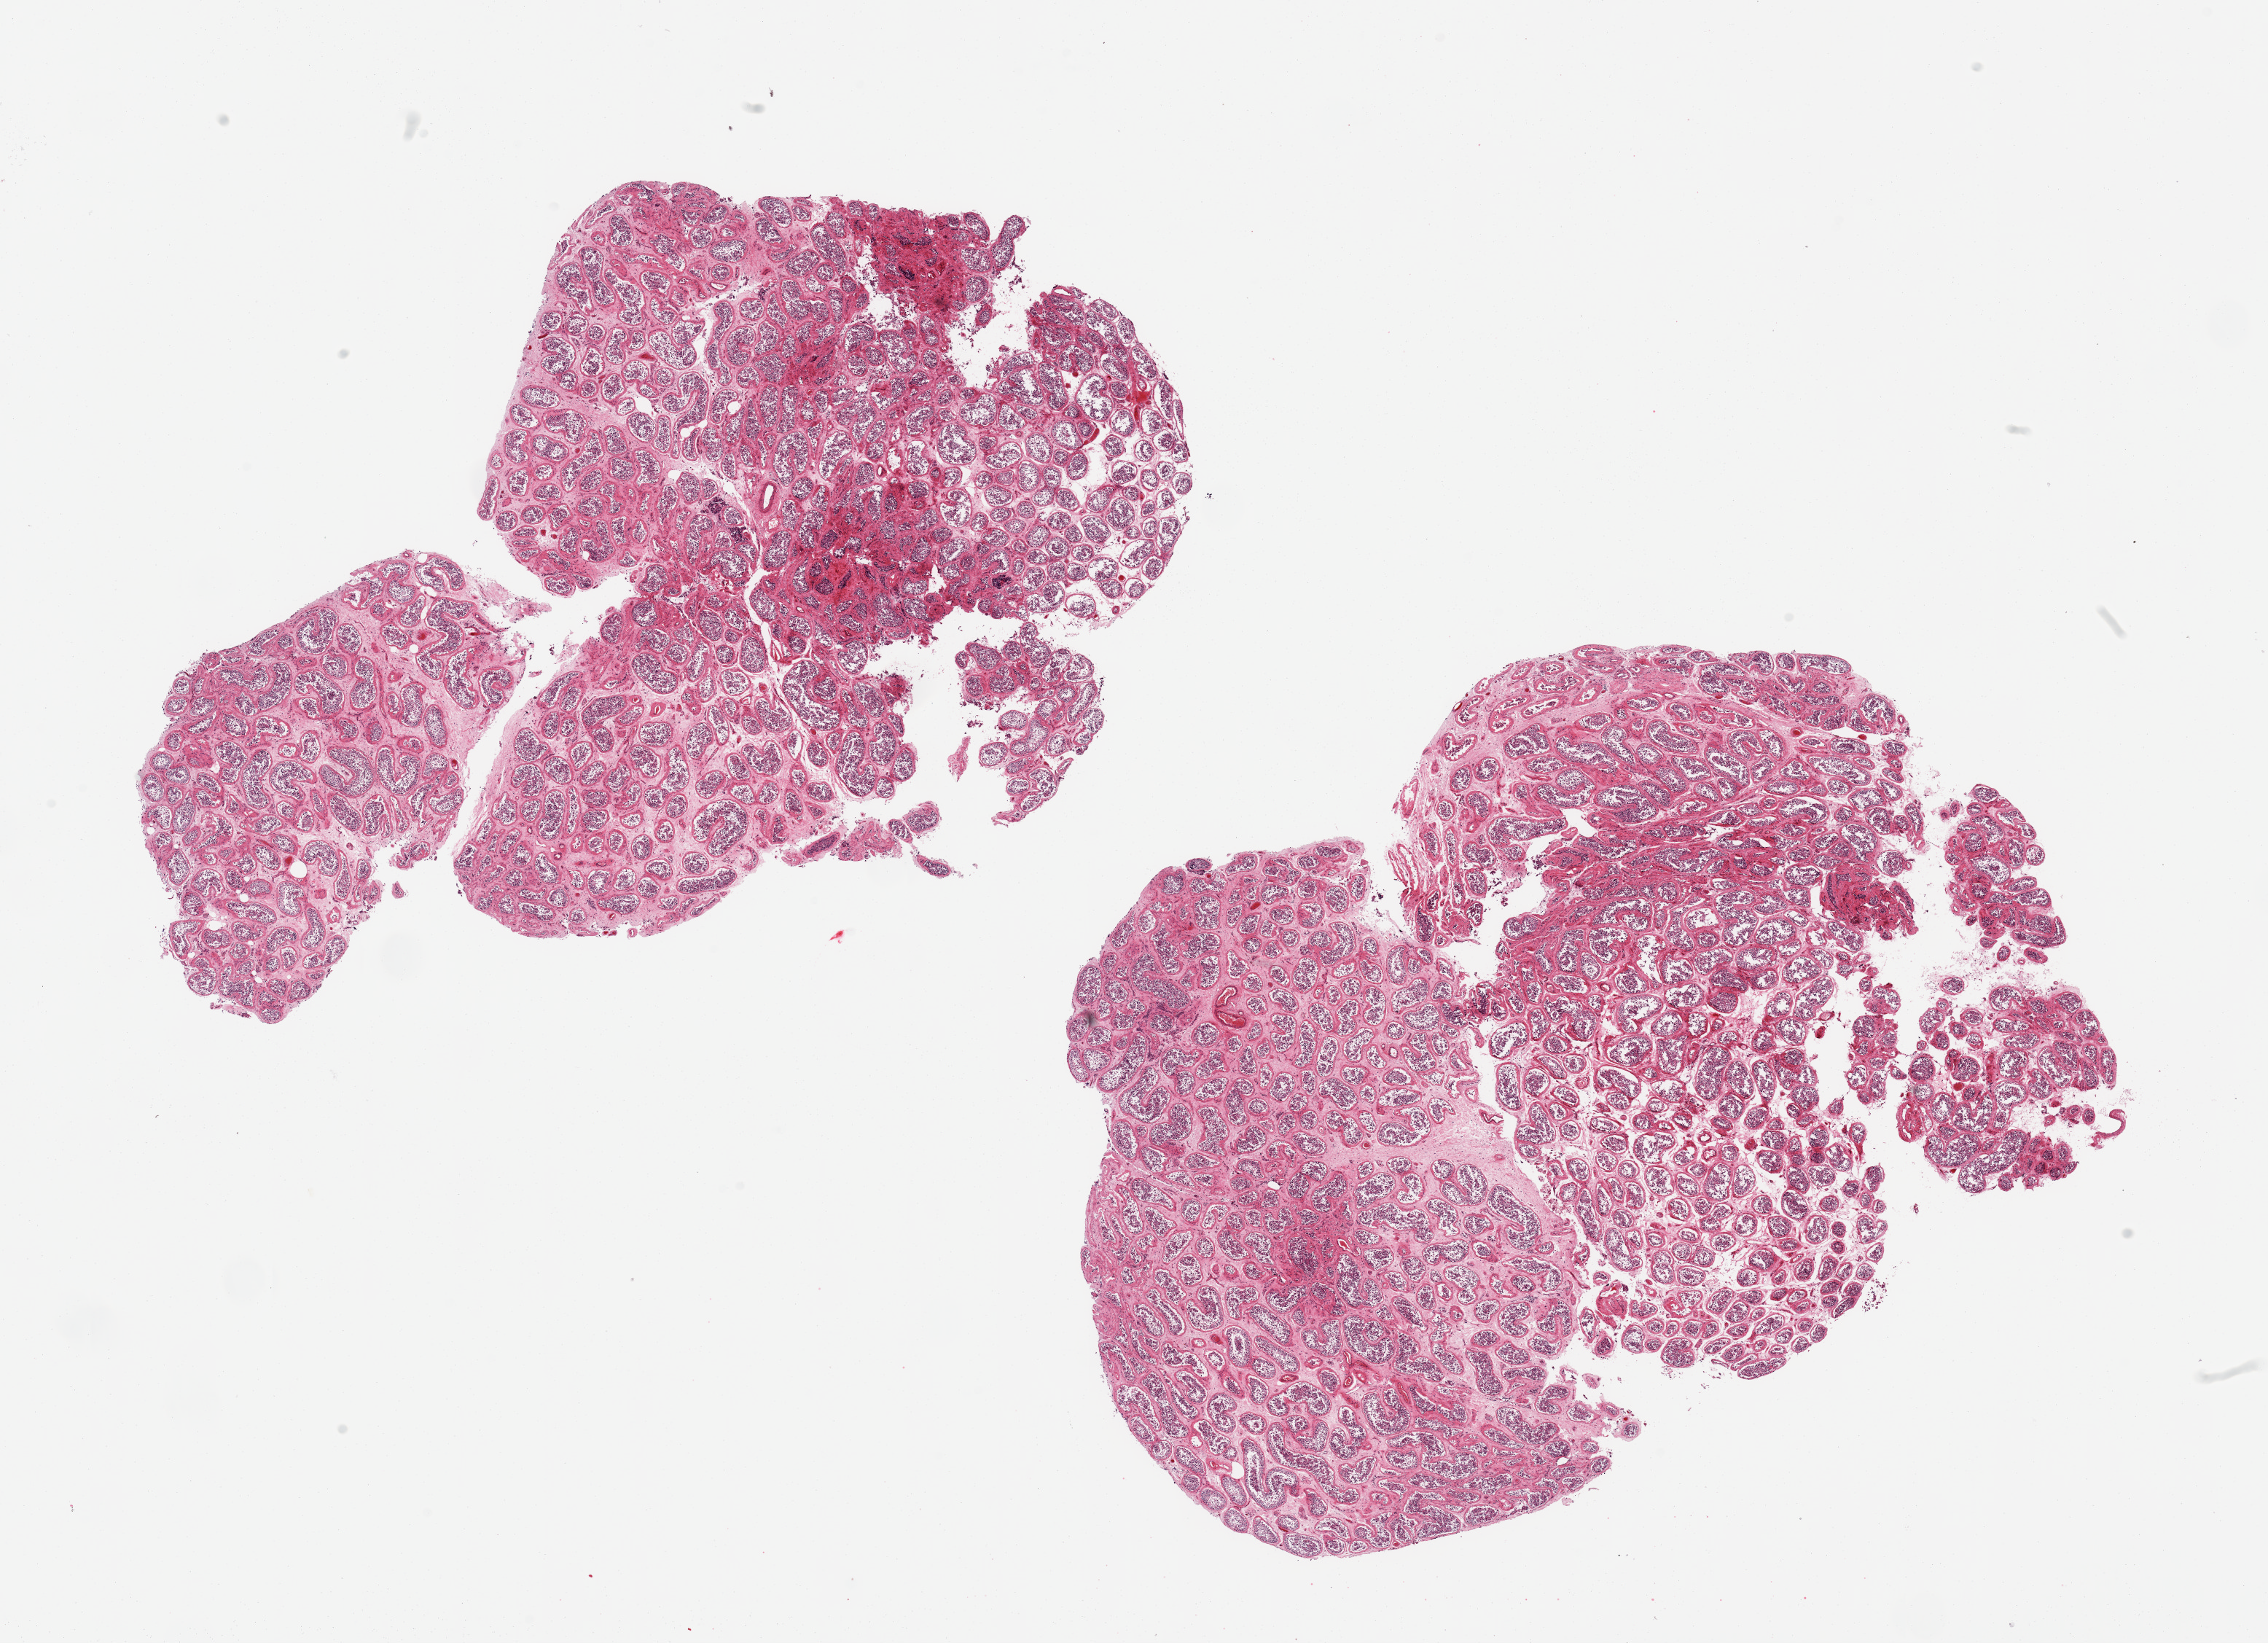
Whole-slide image, H&E stain, a low-resolution overview of the entire scanned area, about 24.6 x 17.8 mm (acquisition: 20x scan). PAXgene-fixed, paraffin-embedded tissue. Sampled site (target tissue): testis. Donor tissue sample. Male donor.
- pathologist's review note for this sample: 2 pieces; spermatogenesis